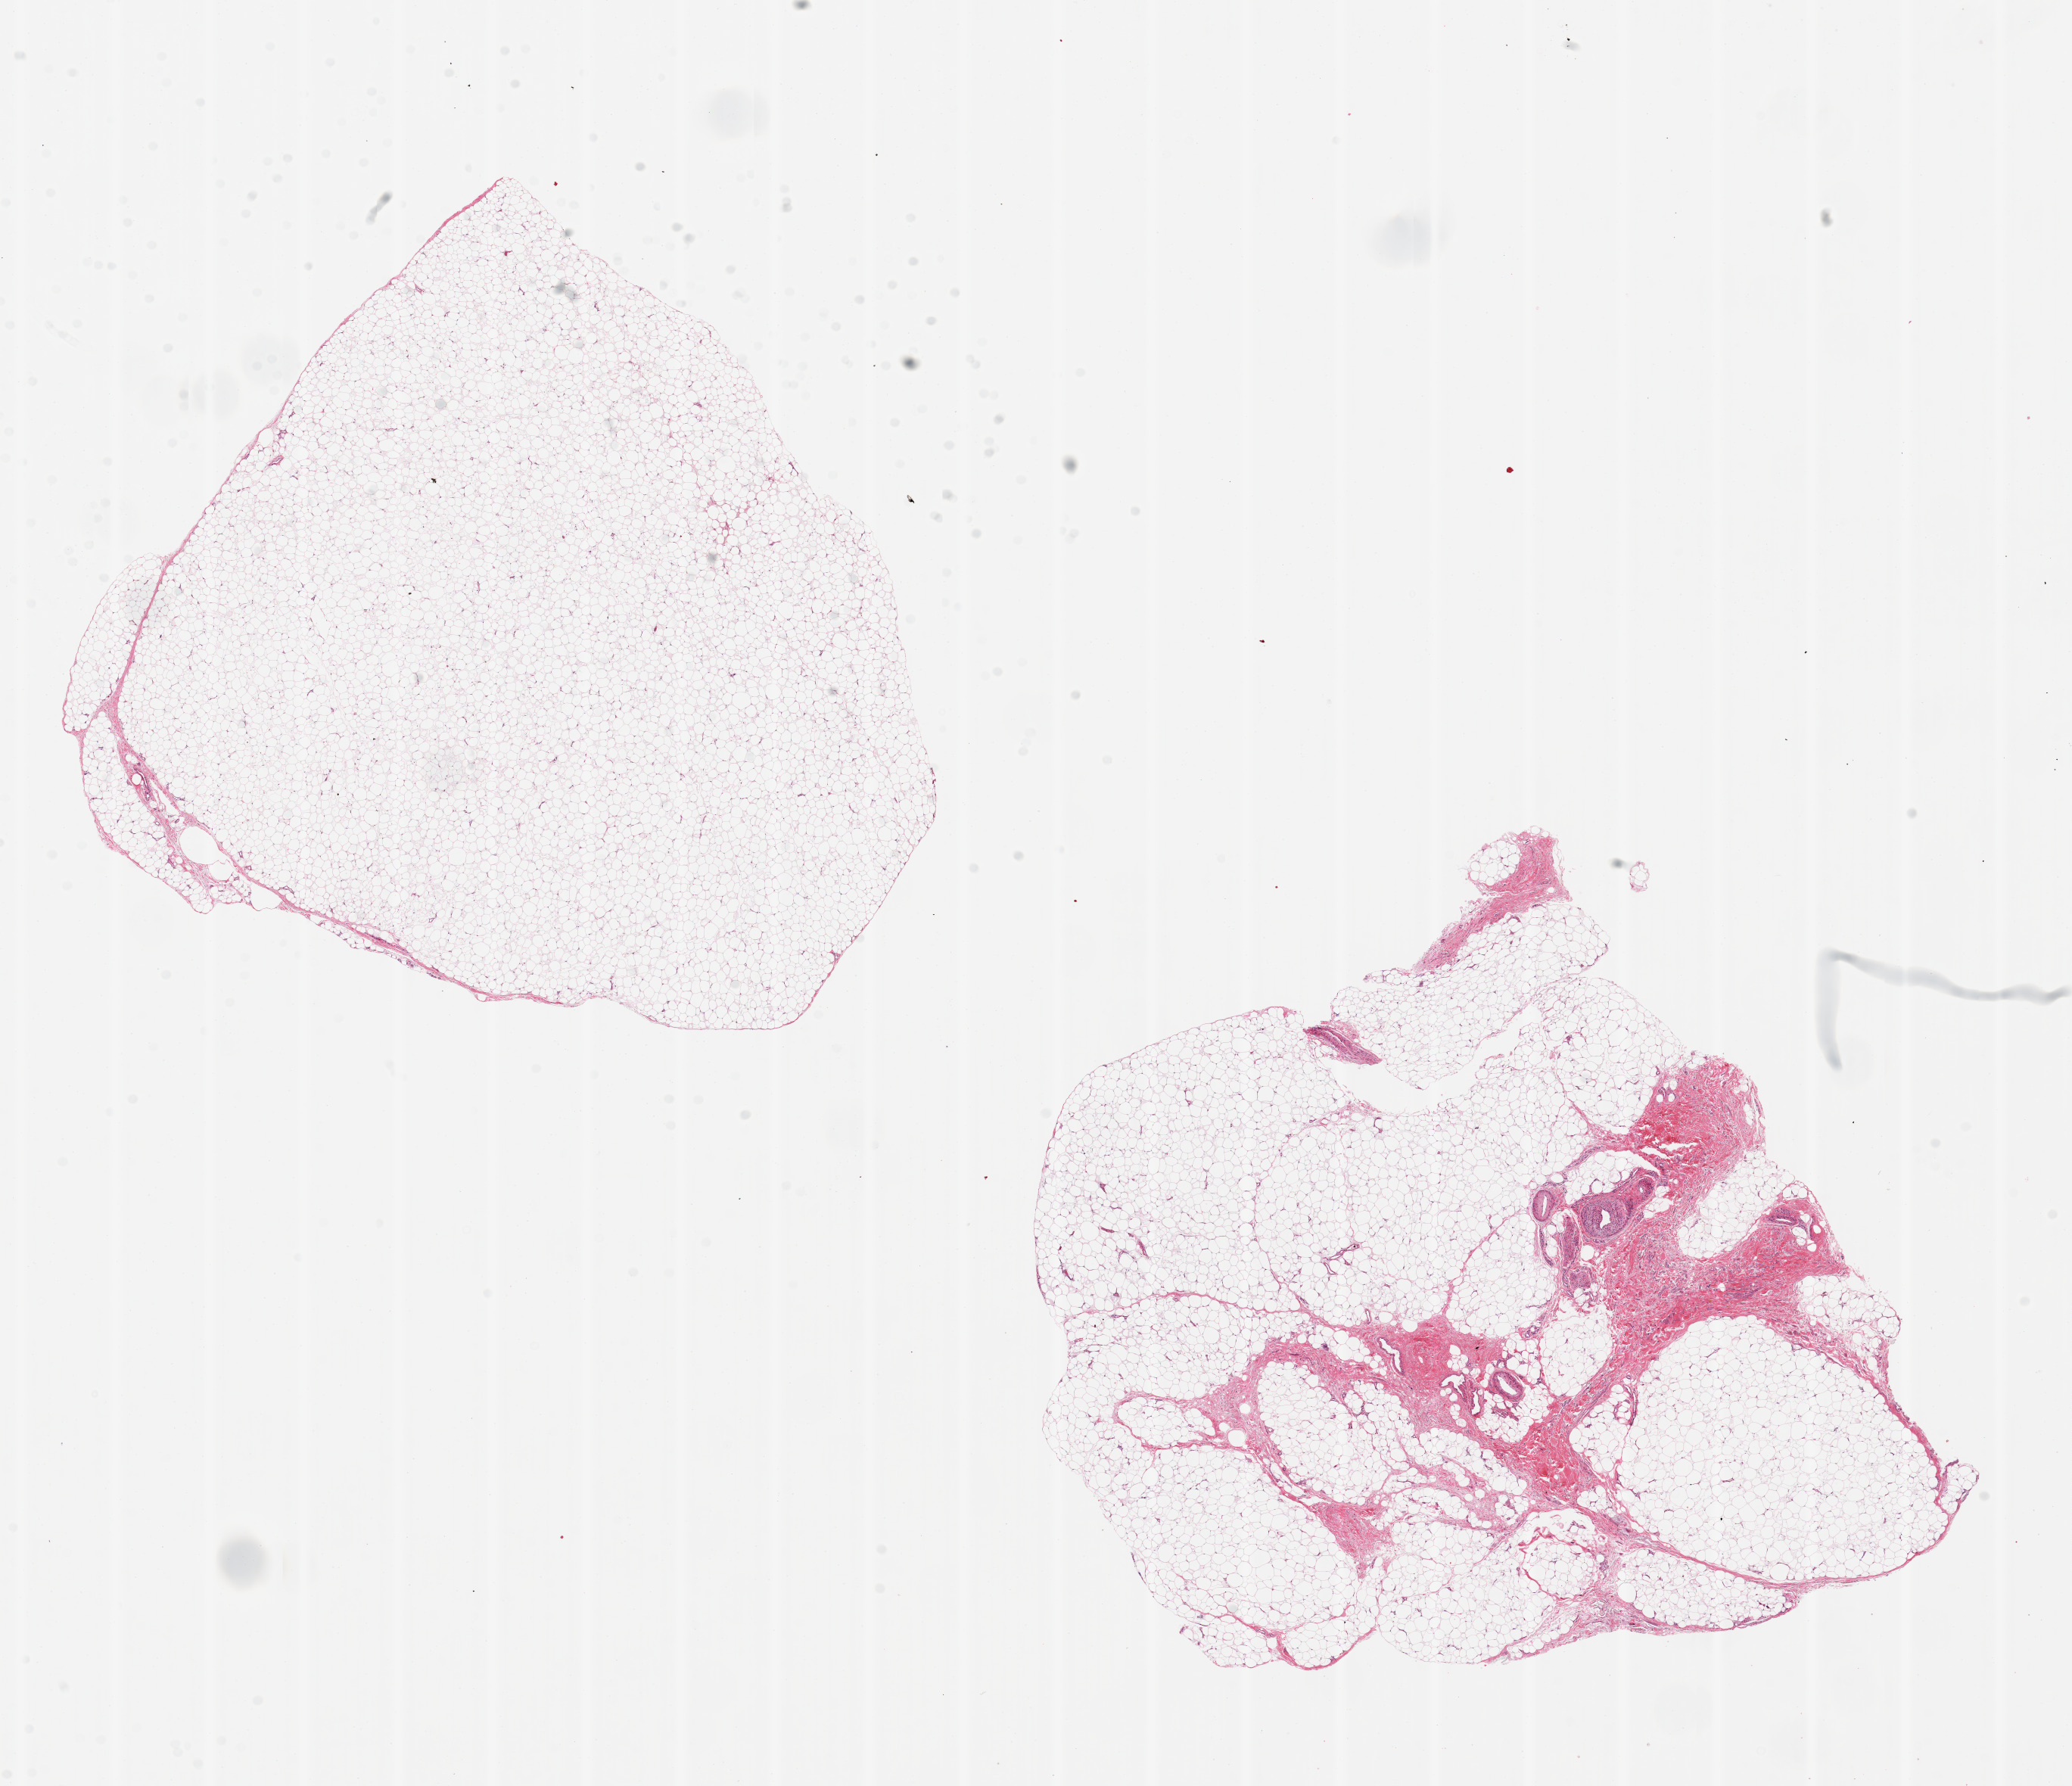
Whole-slide image, H&E stain, a low-resolution overview of the entire scanned area, about 21.7 x 18.7 mm (slide scanned at 20x), PAXgene-fixed paraffin-embedded (PFPE) section, sampled site (target tissue): adipose tissue, donor tissue sample. Male donor.
Review note (as recorded): 2 pieces `7x7mm ~10 fibrous tissue.